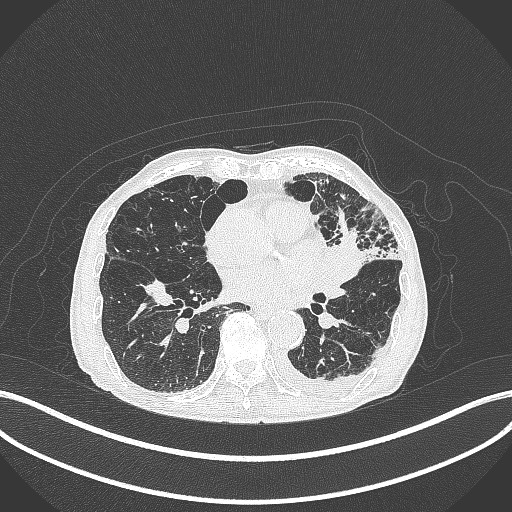
Chest CT, one axial slice. Slice 168 of 385 in the series (ordered by position). Reconstruction kernel B70f. 120 kVp. Lung window (W 1500 / L -600 HU). 1 mm slice thickness. 512 × 512 image matrix, field of view 400 × 400 mm. Male patient, age 90 years or older. From the clinical record (not read from this slice): clinical TNM (as recorded): T2b N1 M0.
Outlined on this slice (bounding box drawn by a radiologist):
- lung tumour (recorded histology: squamous cell carcinoma): box from (x=333, y=237) to (x=380, y=284) px